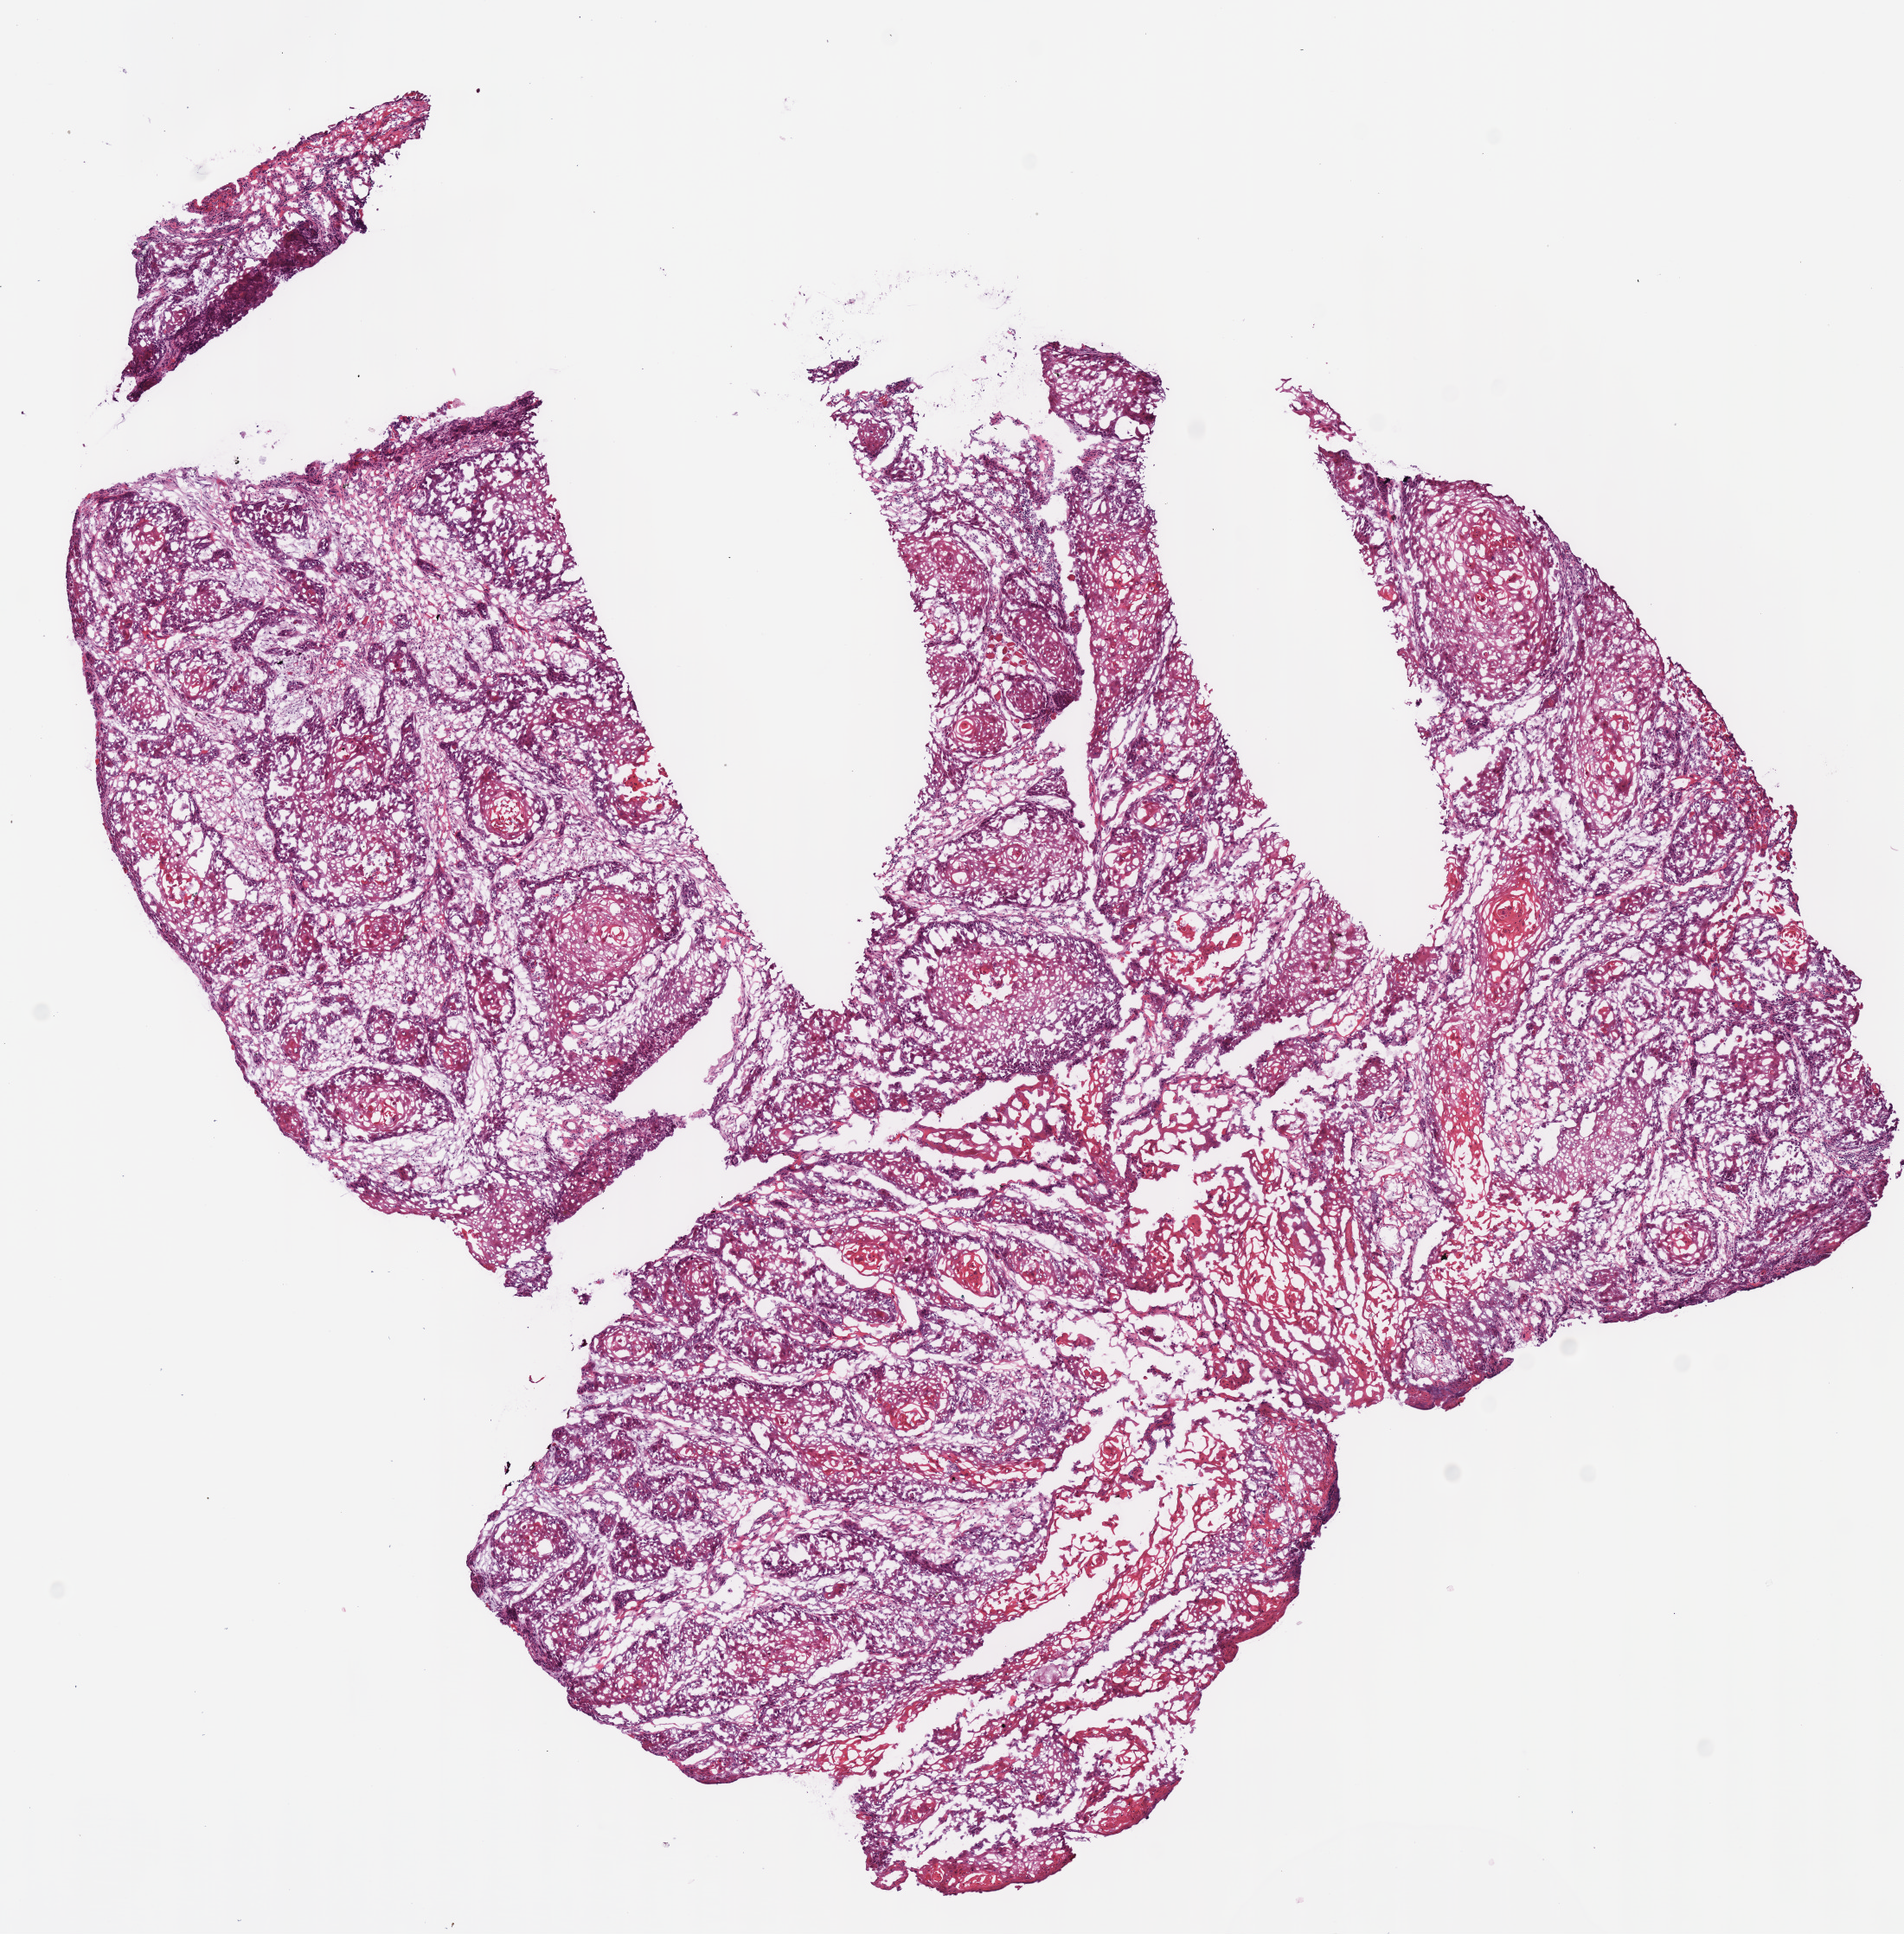
Digitized Hematoxylin and eosin (H&E) stained tissue section (whole slide) — whole scanned area (about 8.7 x 8.8 mm, acquisition: 40x scan) shown as a low-resolution overview. Frozen section from the bottom of the tissue portion. Head and neck, primary tumour sample. Male, age 65 years at initial diagnosis. Histologic grade: G1 (well differentiated). Slide review estimates, as recorded: tumour cells 100%, tumour nuclei 78%, normal cells 0%, stromal cells 0%, necrosis 0%. Infiltration values recorded for this section: lymphocyte infiltration 10%, monocyte infiltration 0%, neutrophil infiltration 2%.
AJCC pathologic stage: II (7th edition). Pathologic diagnosis: Squamous cell carcinoma, NOS (overlapping lesion of lip, oral cavity and pharynx).